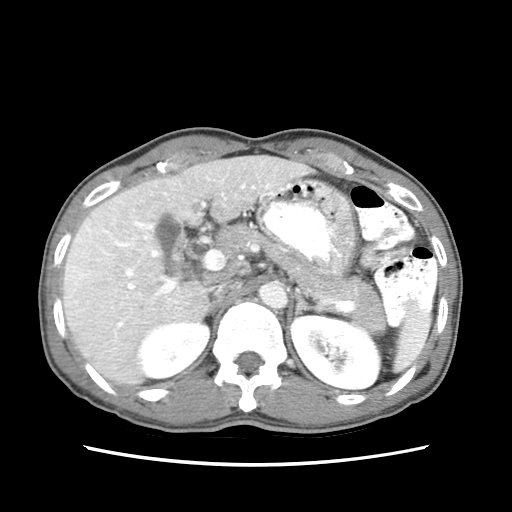
Contrast-enhanced abdominal CT (liver protocol), one axial slice. Soft-tissue window (W 400 / L 40 HU). 2.5 mm slice thickness. 512 × 512 image matrix. From the clinical record (not read from this slice): diagnosis: hepatocellular carcinoma (patient treated with transarterial chemoembolisation; whether this scan precedes or follows treatment is not stated here); TNM stage (as recorded): Stage-IIIB; Child-Pugh class: A; tumour differentiation: moderately differentiated; tumour nodularity: multinodular.
Annotated regions visible in this slice (semi-automatically segmented with operator editing):
- liver parenchyma outside the tumour (the mass and vessels are separate outlines, so this box may not span the whole liver): bounding box <64,154,314,392> (left, top, right, bottom; pixels)
- mass: <65,241,110,286>
- liver vessels: <65,161,300,339>